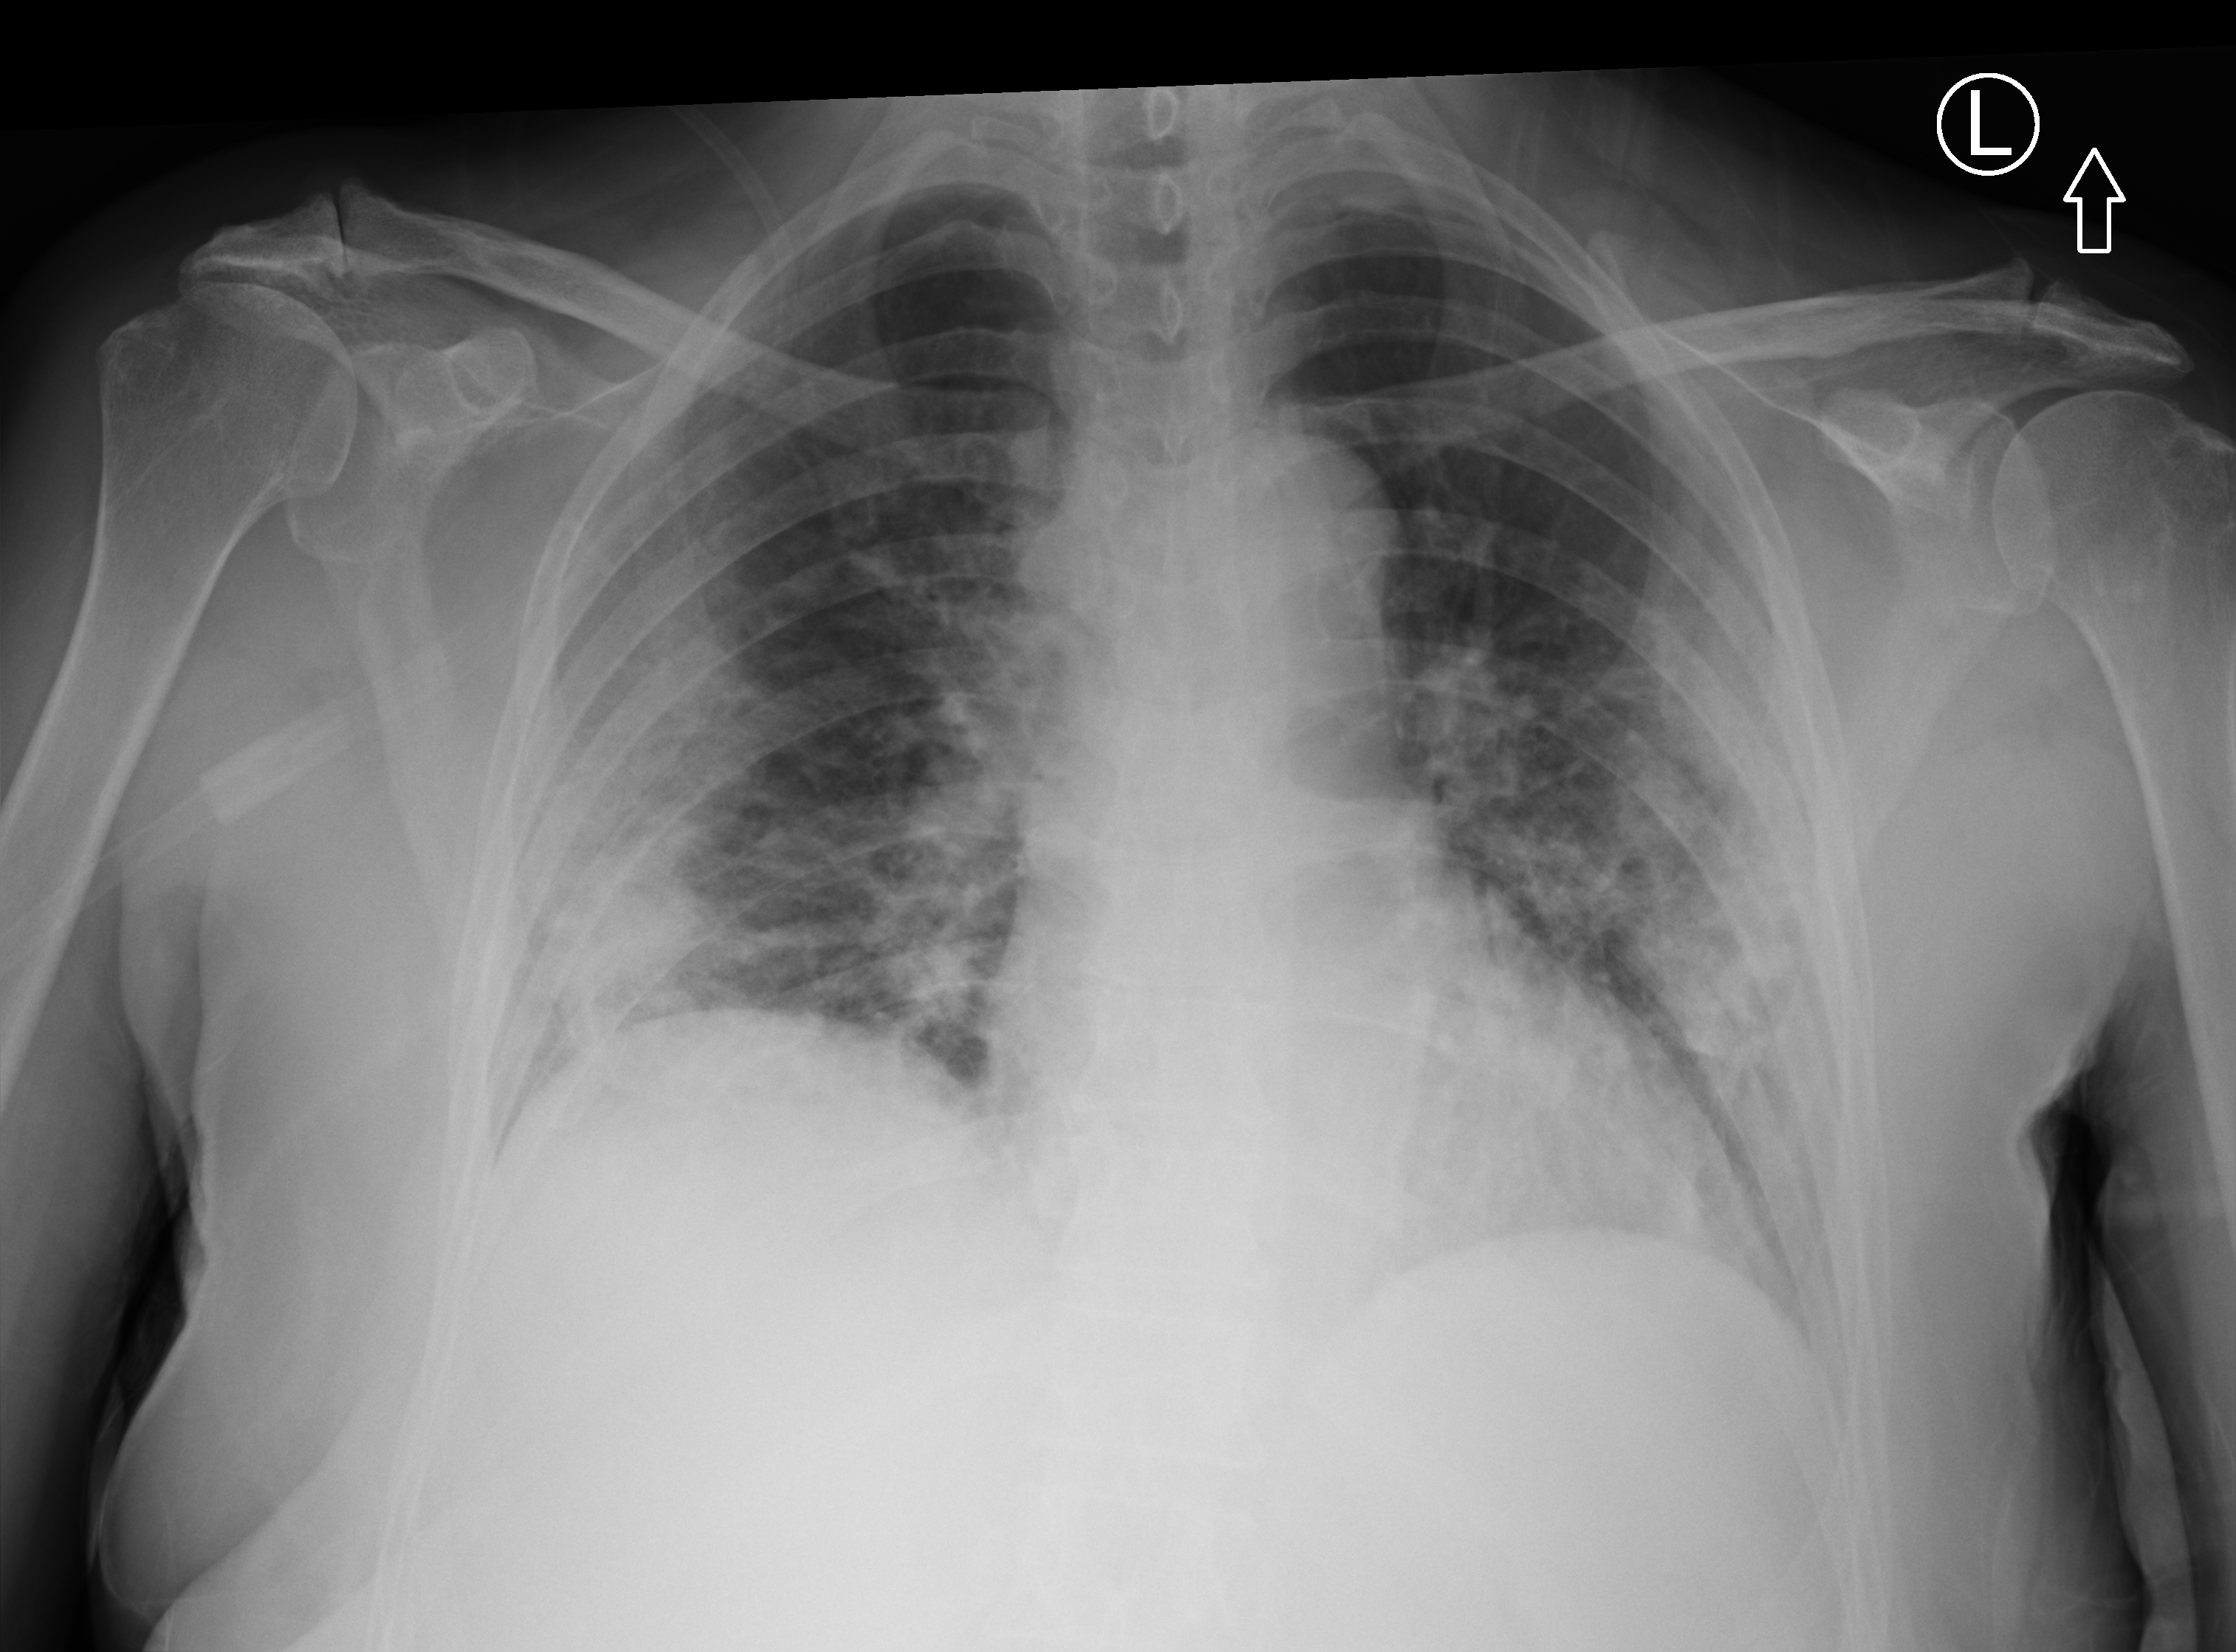
Bedside chest radiograph (computed radiography), anteroposterior (AP) projection. Female patient hospitalised with COVID-19, age 60–74 years.
From the hospital-stay record, not from the radiograph (when in the stay this image was taken is not recorded): mechanically ventilated during this hospital stay: yes; diabetes (admission record): no; smoking status (admission record): former.